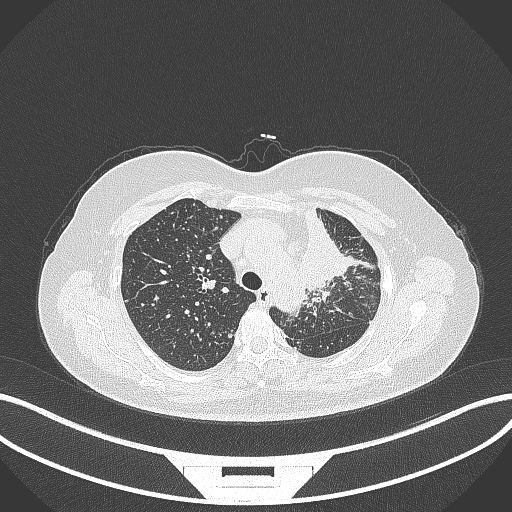
Chest CT, one axial slice; position 250 of 348 along the scan axis; 120 kVp; lung window (W 1500 / L -600 HU); 512 × 512 image matrix. Patient: female, 49 years. From the clinical record (not read from this slice): clinical TNM (as recorded): T1c N0 M1.
Structures marked on this image (rectangle marked by the reading radiologist):
- lung tumour (recorded histology: adenocarcinoma): bounding box [x1, y1, x2, y2] px = [292, 206, 355, 299]